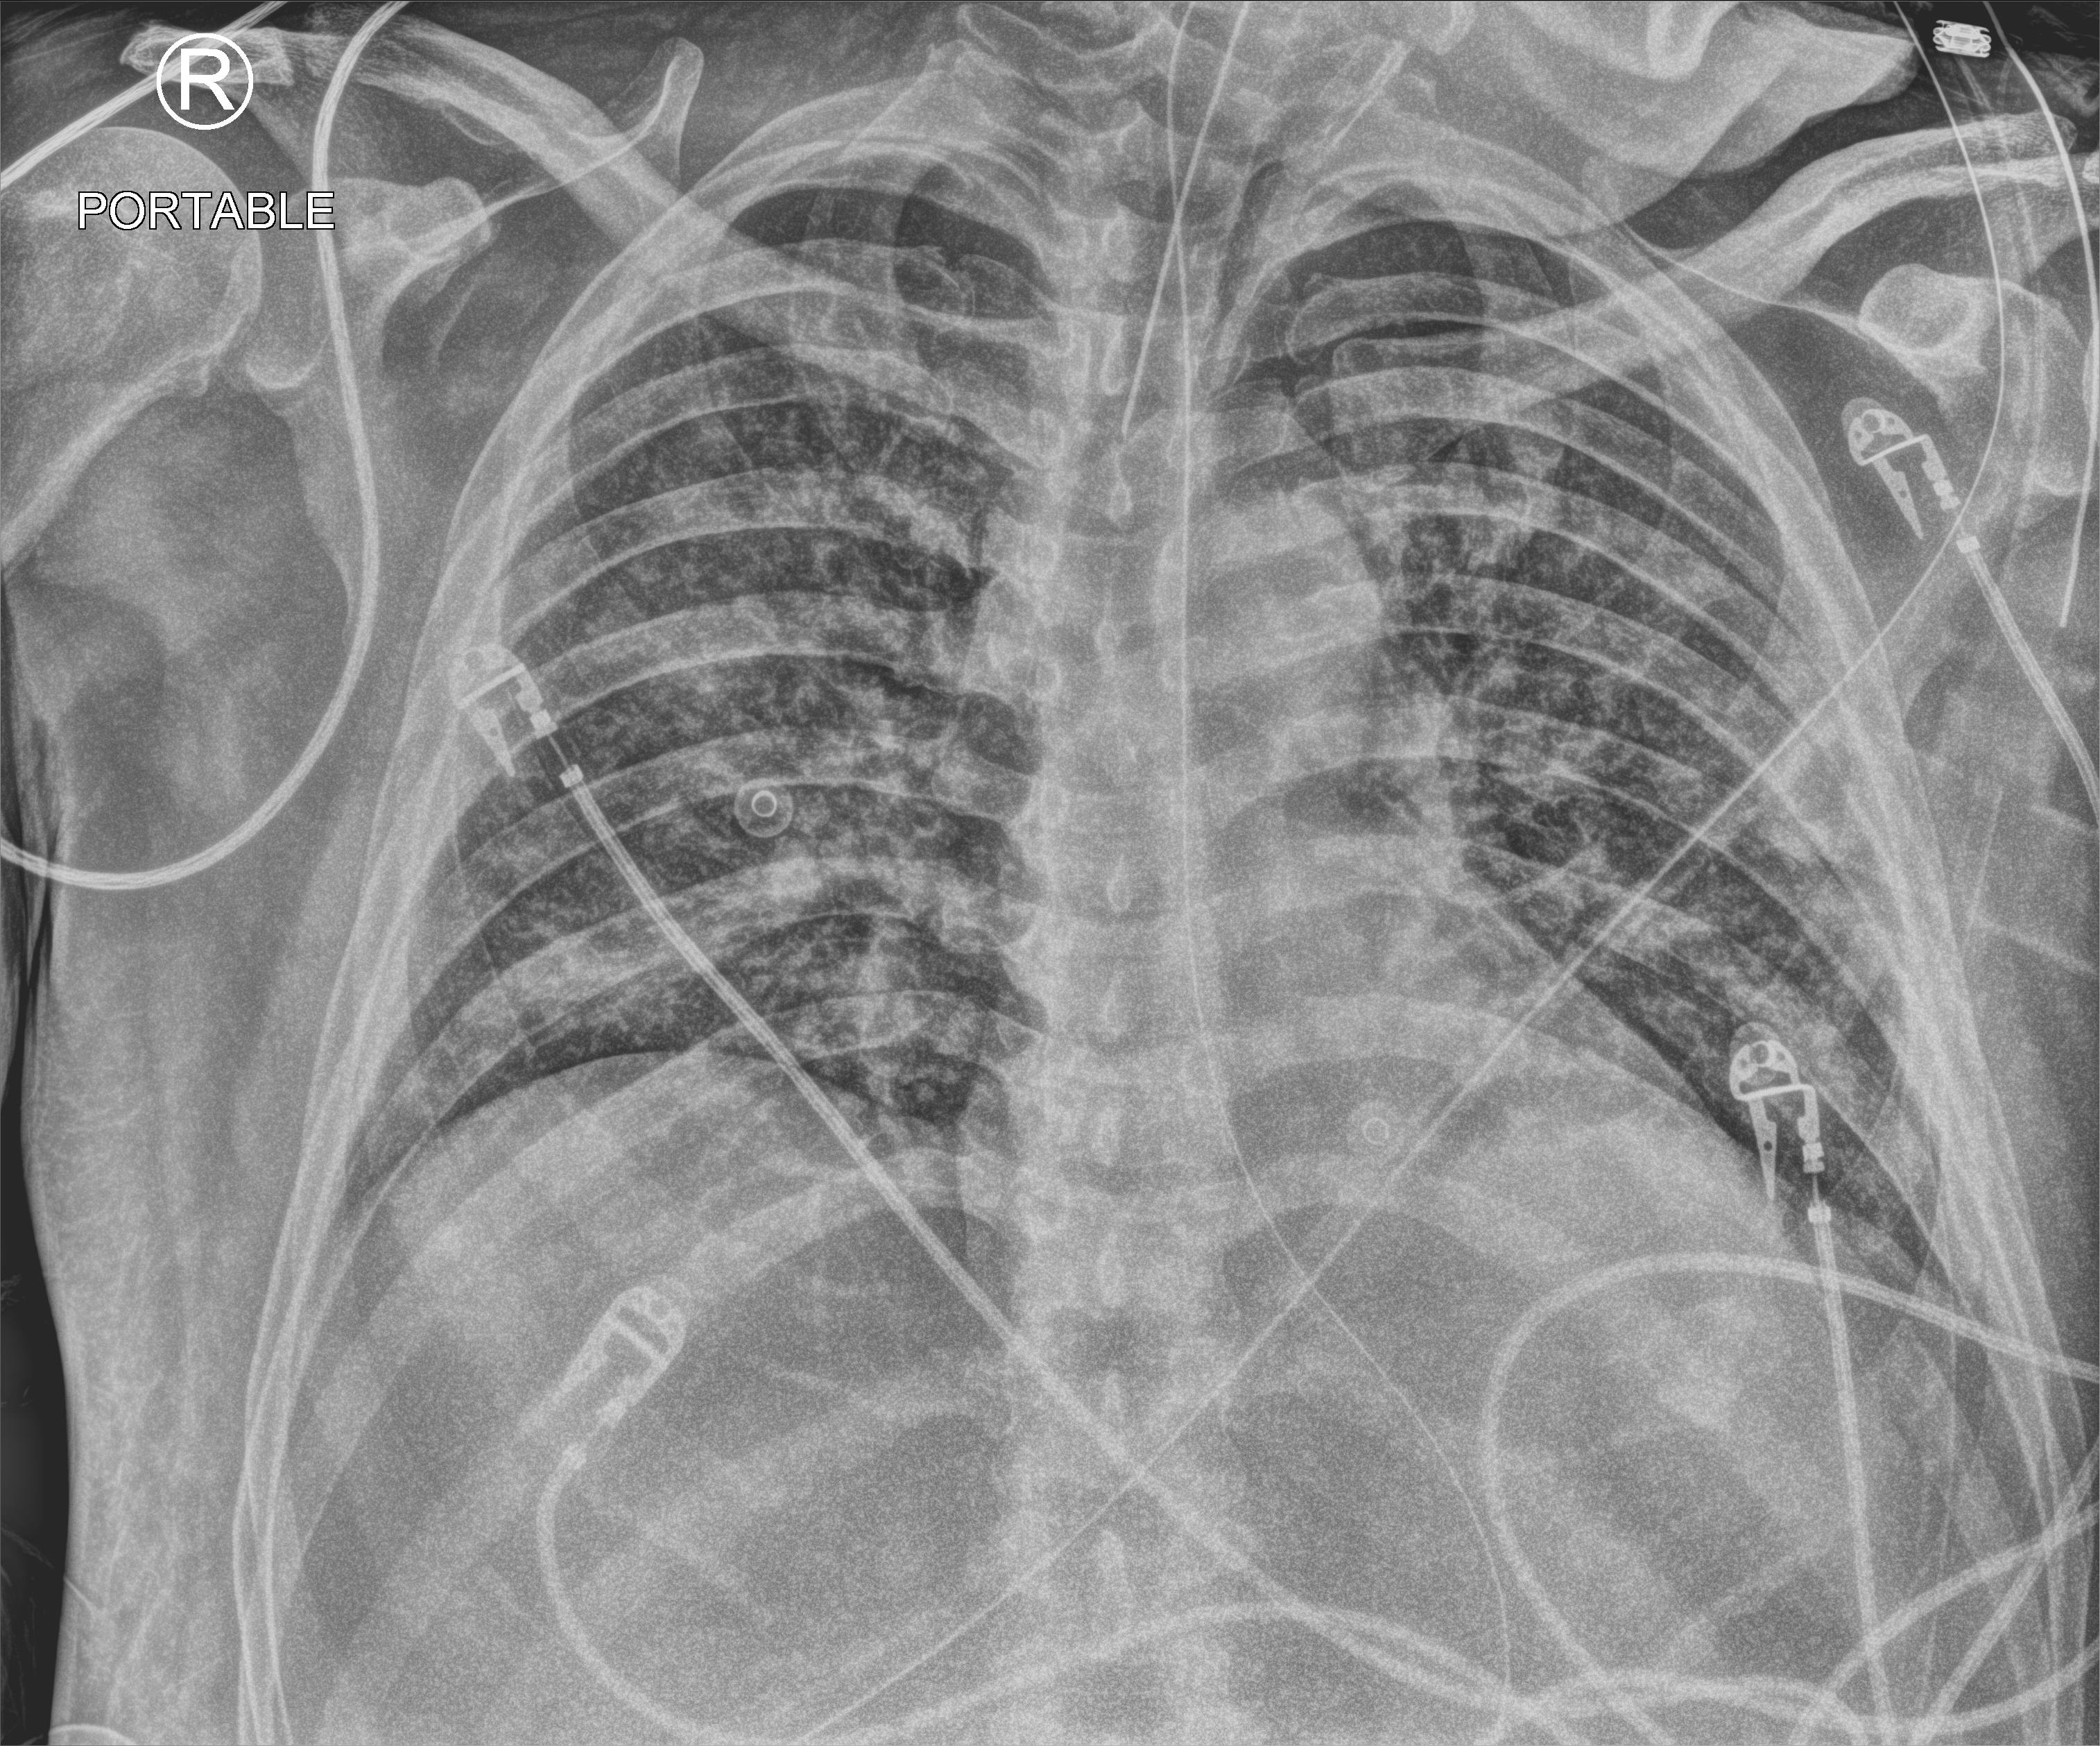
Chest X-ray (portable). Patient hospitalised with COVID-19; male, aged 18–59 years.
Admission-level facts for this patient (not findings on this image; timing relative to this image not recorded):
- mechanically ventilated during this hospital stay: yes
- admitted to intensive care during this hospital stay: yes
- smoking status (admission record): never